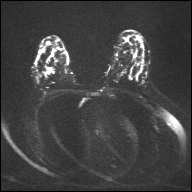
Breast MRI, one axial slice; slice 23 of 32 in the series (ordered by position); diffusion-weighted series; image 2 of 4 stored at this slice position (different b-values; order by instance number); 1.5 T; 192 × 192 image matrix, field of view 360 × 360 mm. Female patient.
Structures marked on this image (outlined manually by an expert reader):
- tumour on diffusion-weighted imaging: bounding box (x1, y1, x2, y2) in pixels: (47, 68, 51, 73)